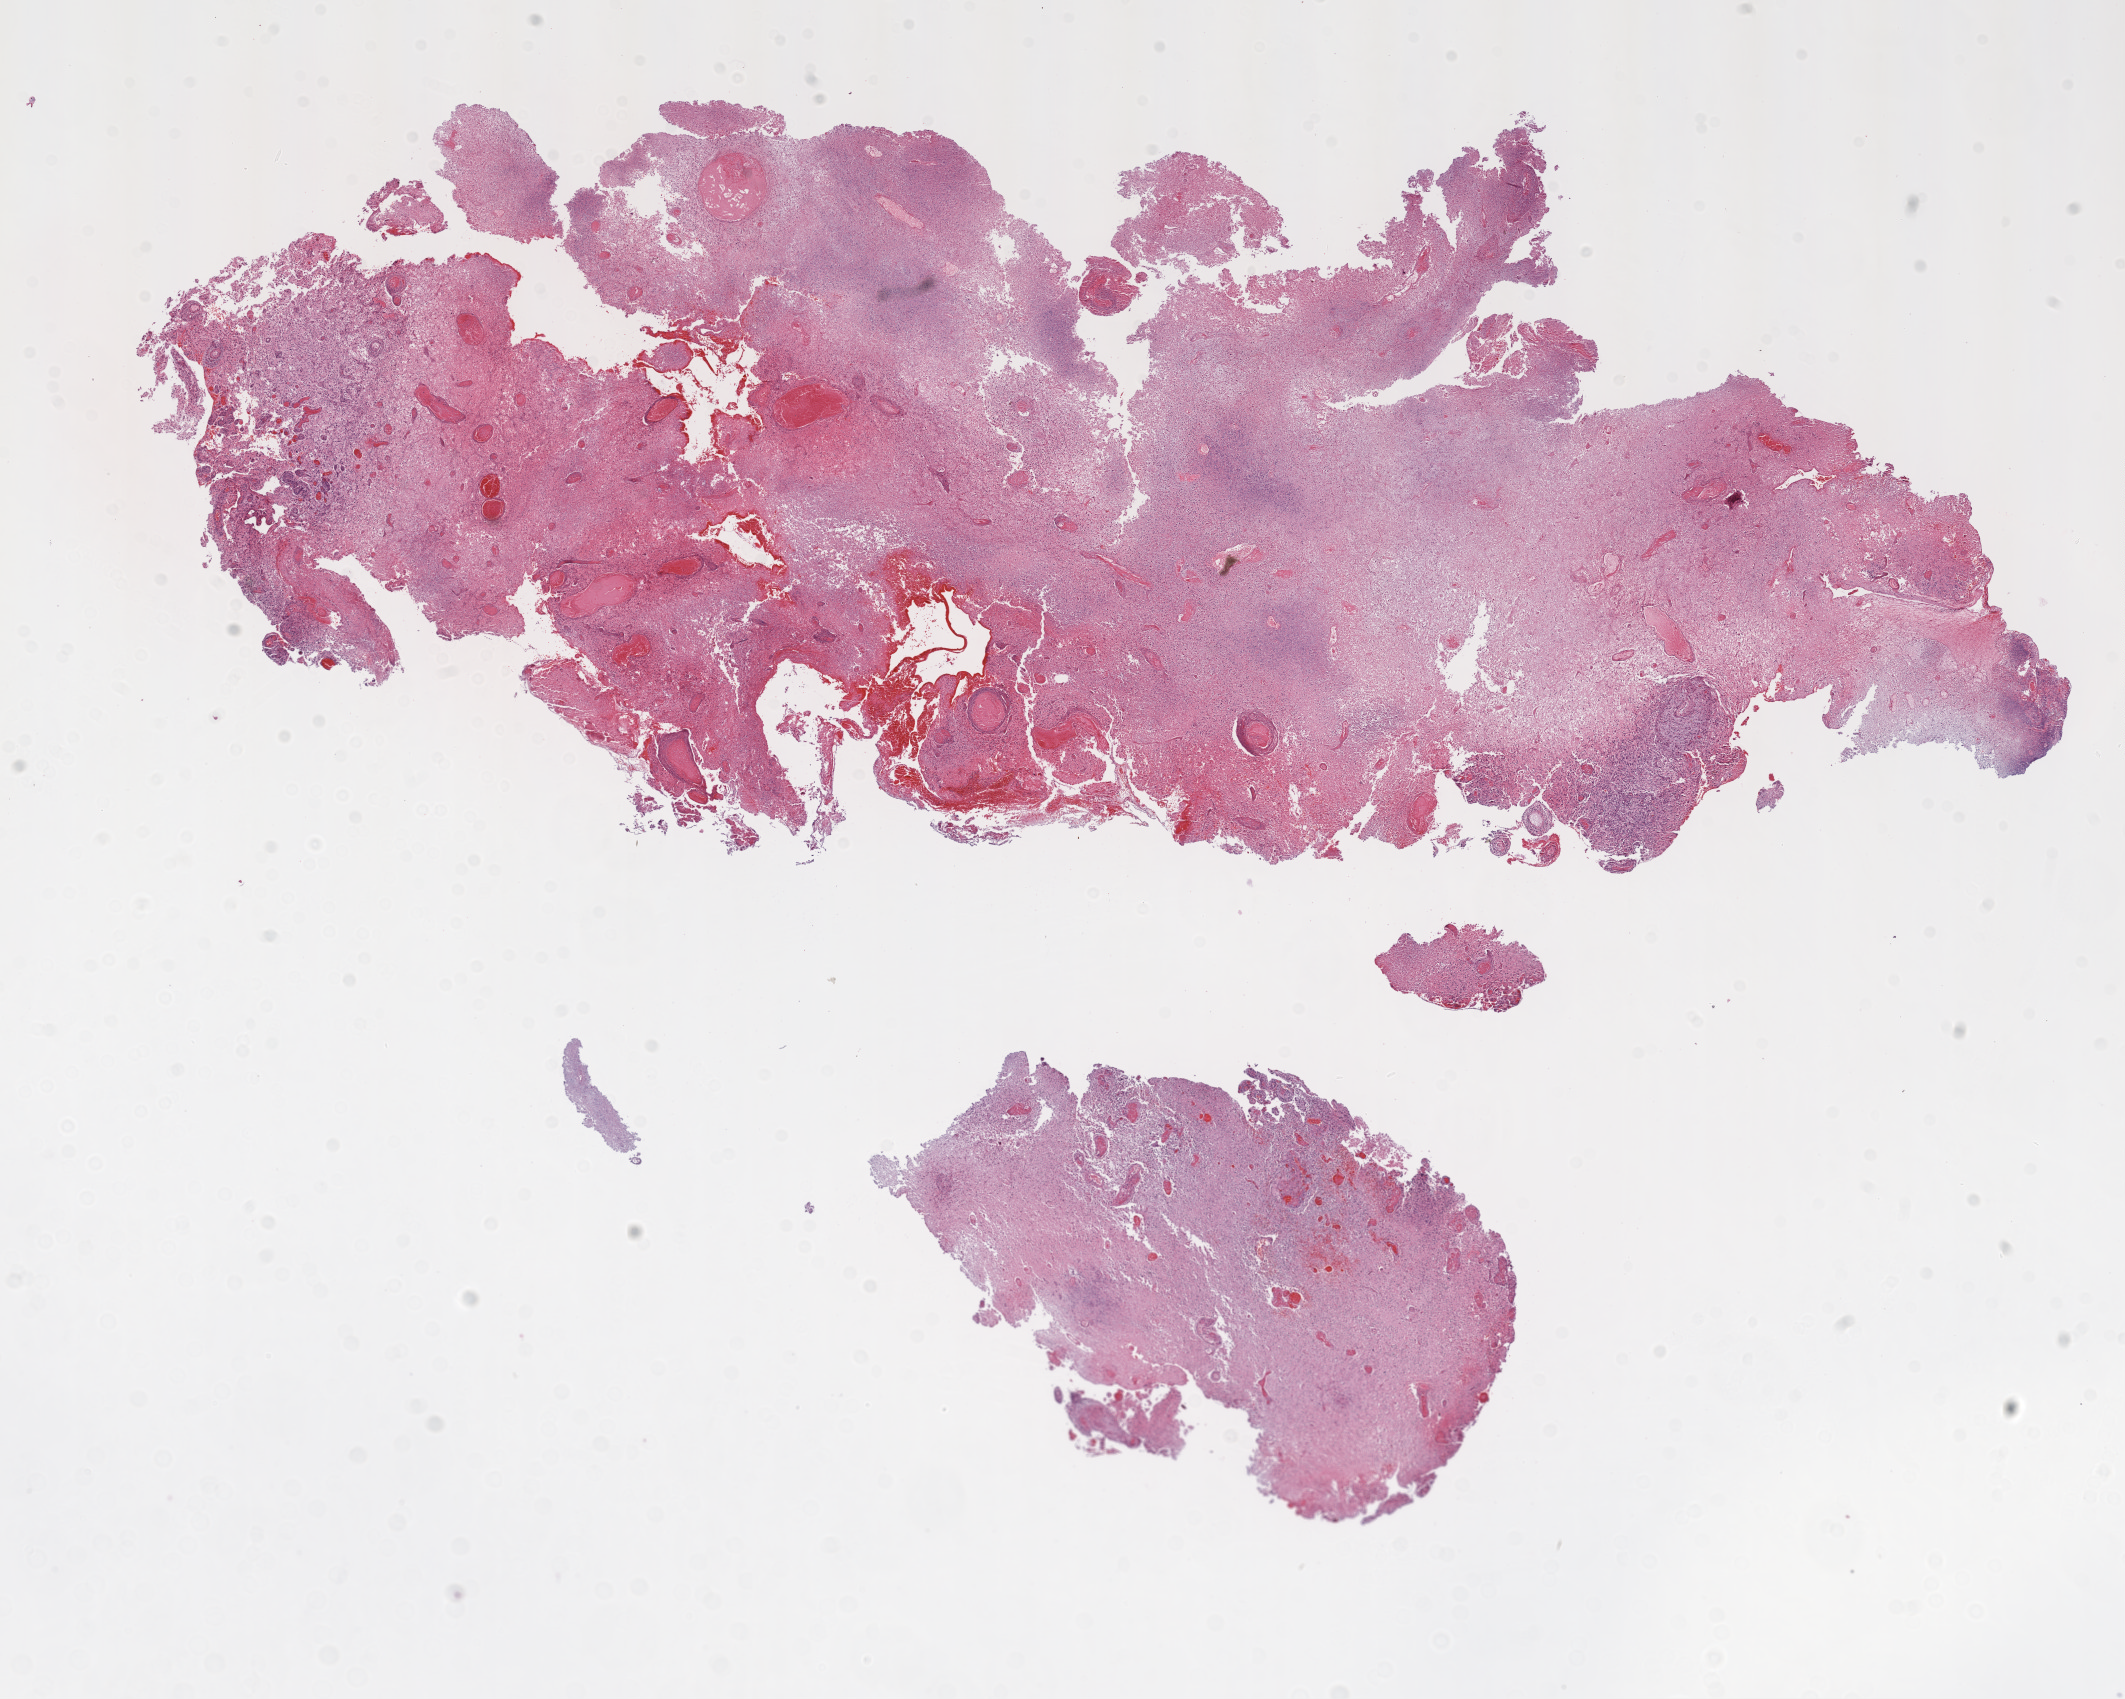
H&E-stained whole-slide image — low-resolution overview of the scanned area, about 17.1 x 13.6 mm; FFPE section; primary tumour sample from the brain. Male patient; age at initial diagnosis 40 years.
- diagnosis: Glioblastoma